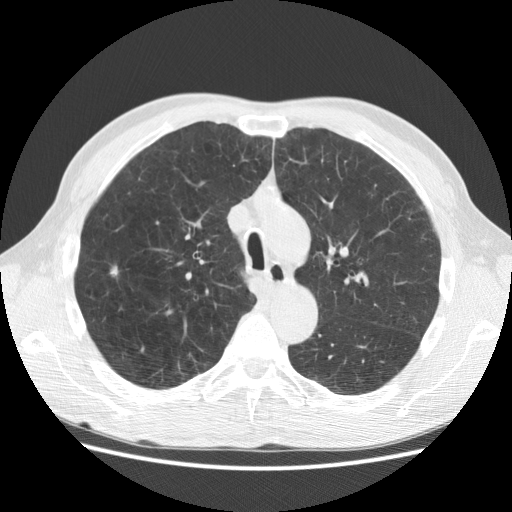
Low-dose screening chest CT, one axial slice. 120 kVp. Lung window (W 1500 / L -600 HU). 2.5 mm slice thickness. 512 × 512 image matrix, field of view 367 × 367 mm.
Structures marked on this image (expert manual segmentation):
- lesion 1 (tumor, upper lobe of right lung): bounding box [x1, y1, x2, y2] px = [111, 267, 118, 275]